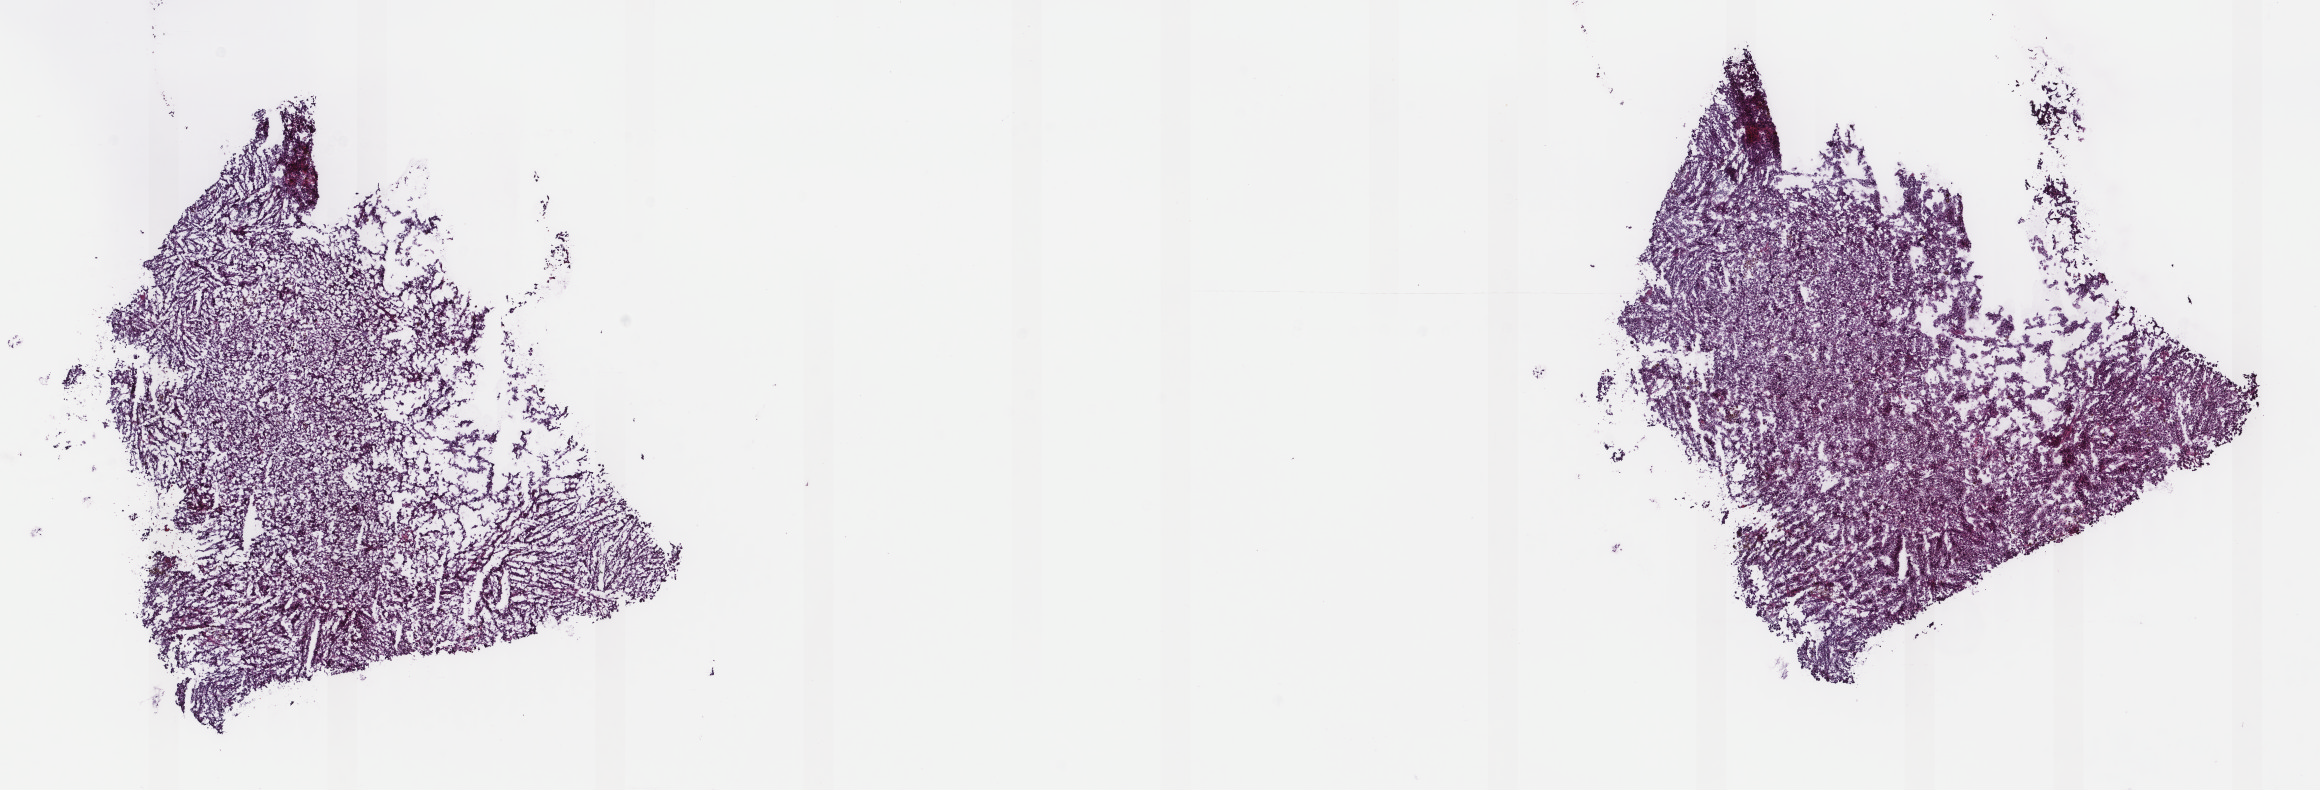
H&E-stained whole-slide image, shown as a low-resolution overview of the whole scanned area (about 18.4 x 6.3 mm); frozen section from the top of the tissue portion; metastatic tumour sample, sampled site not recorded. Female, age 32 years at initial diagnosis. Composition of this section per pathologist review: tumour cells 100%, tumour nuclei 95%, normal cells 0%, stromal cells 0%, necrosis 0%. Infiltration values recorded for this section: lymphocyte infiltration 0%, monocyte infiltration 0%, neutrophil infiltration 0%.
This section: metastatic tumour tissue. Patient diagnosis: Malignant melanoma, NOS.